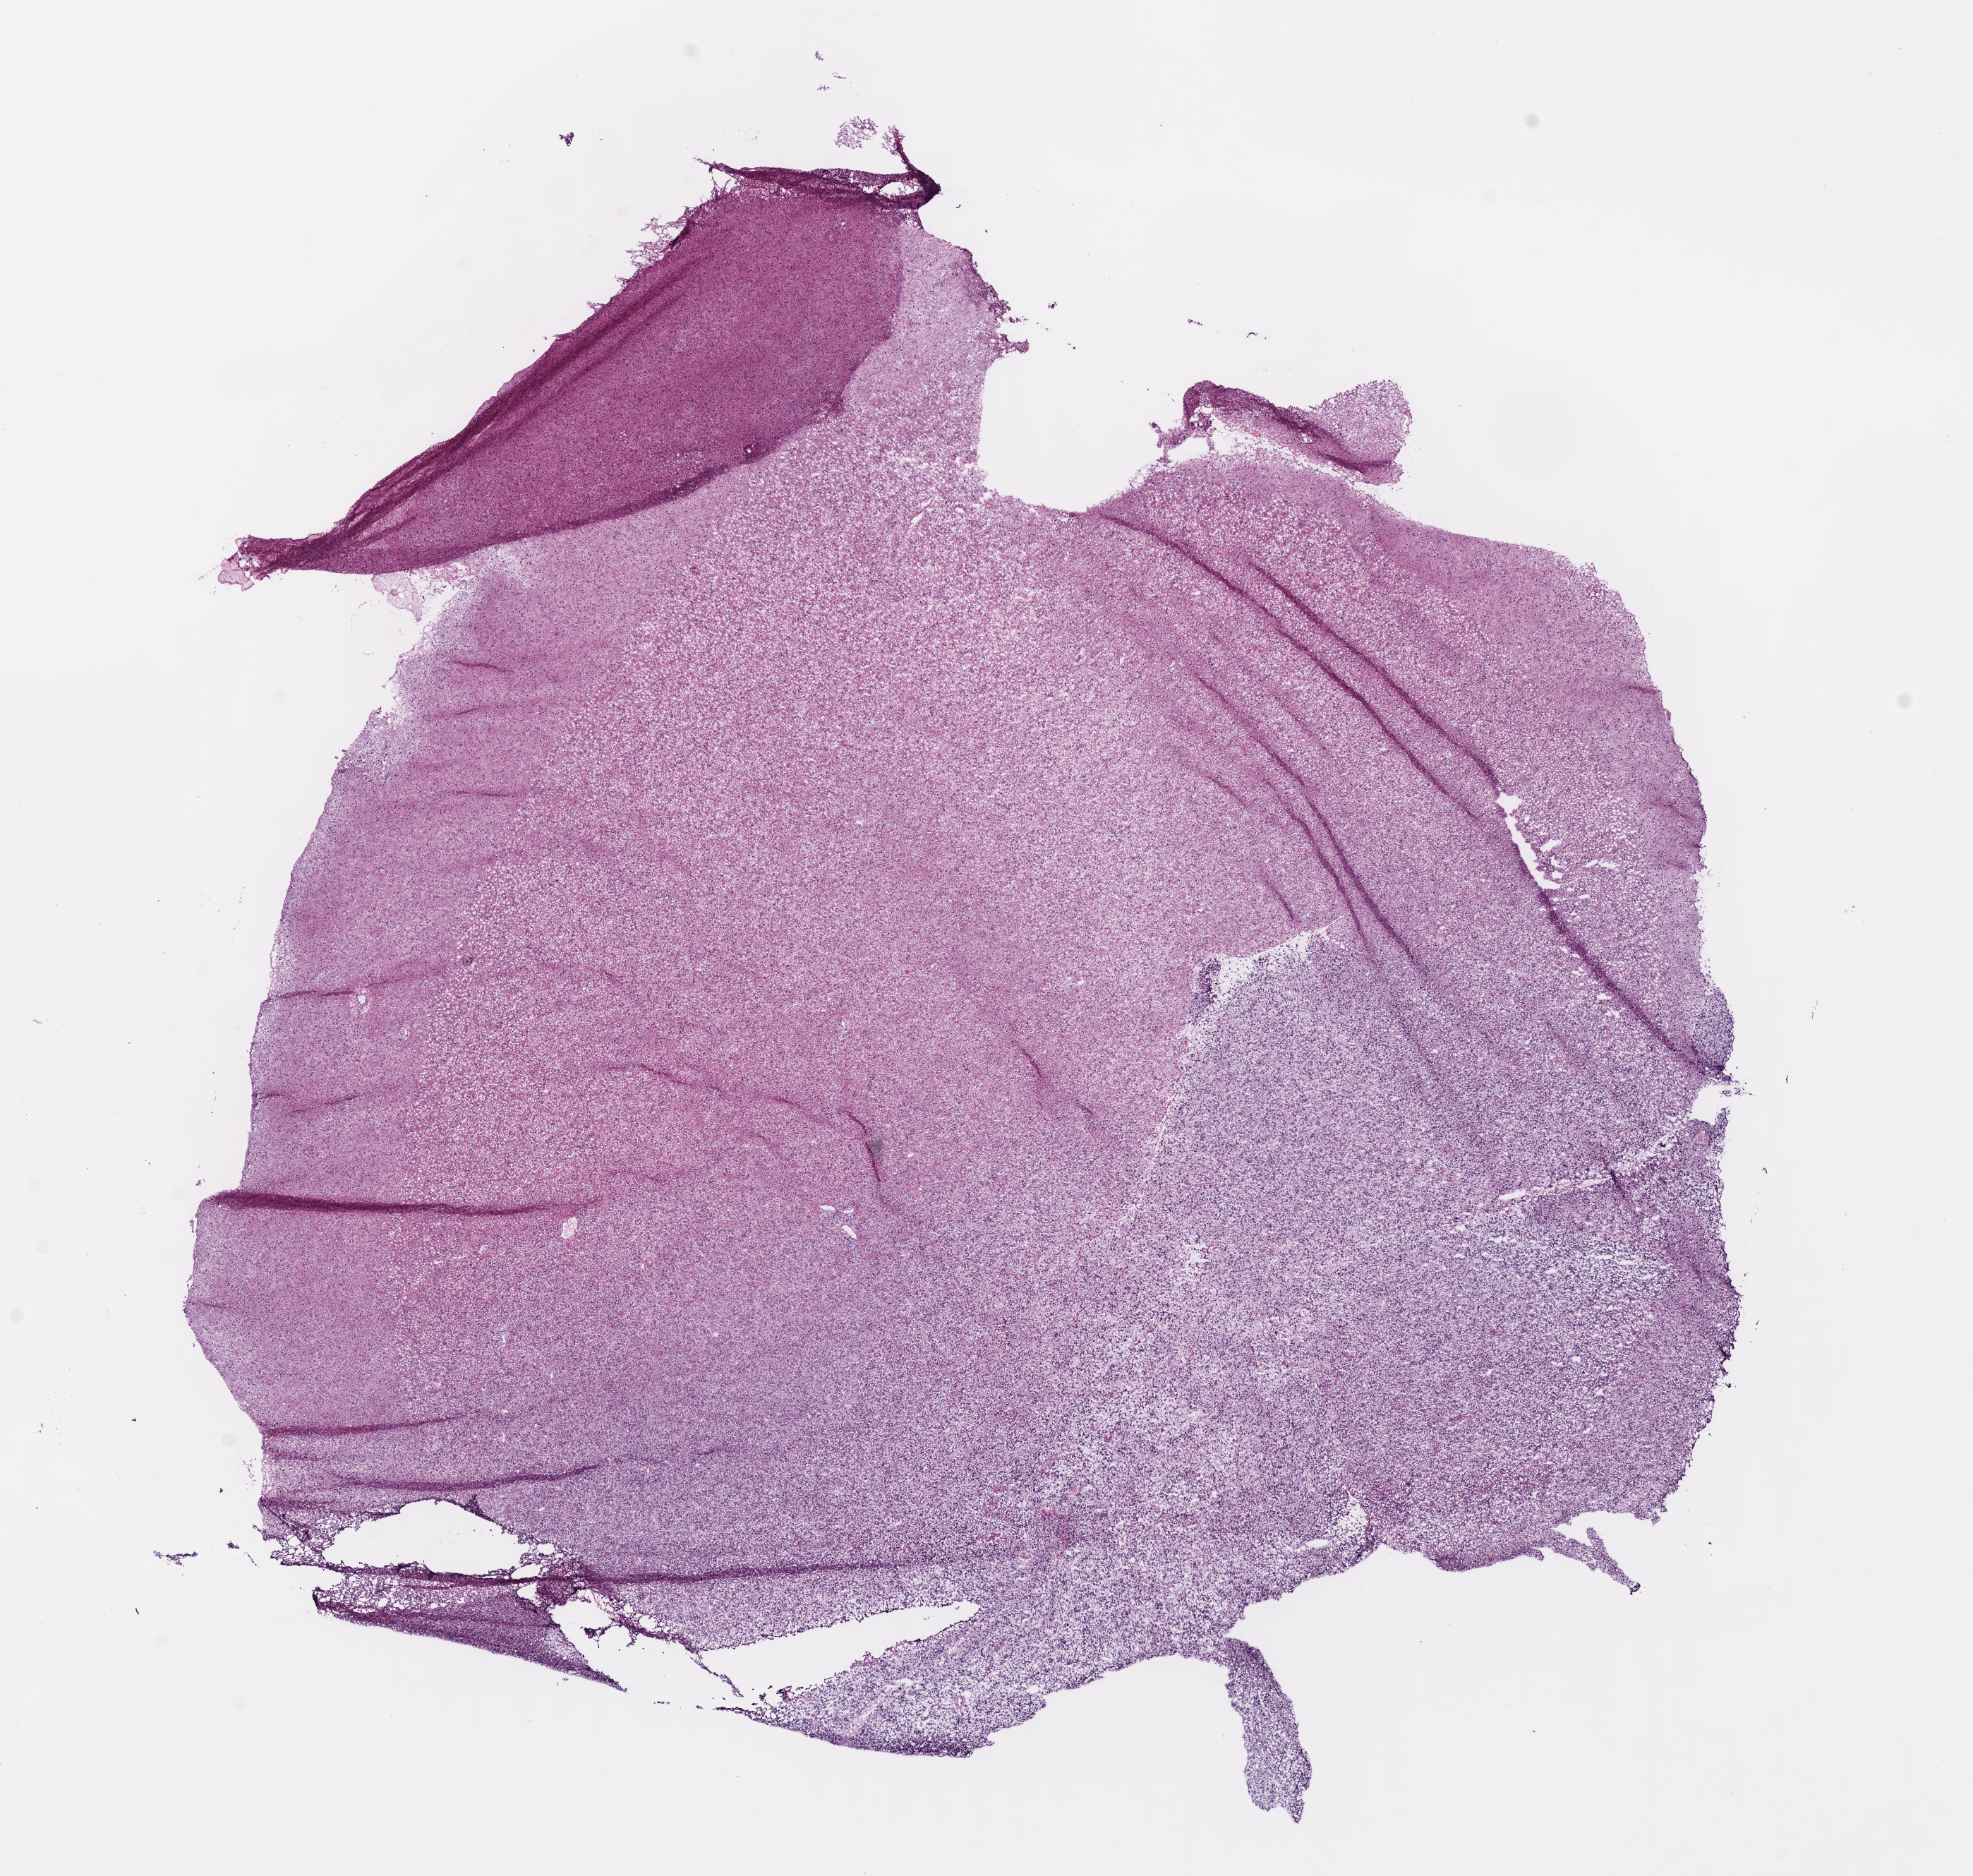
Digitized Hematoxylin and eosin (H&E) stained tissue section (whole slide), shown as a low-resolution overview of the whole scanned area (about 11.0 x 10.5 mm), frozen section from the bottom of the tissue portion, brain, primary tumour sample. Female, age 30 years at initial diagnosis. Histologic grade: G2 (moderately differentiated). Pathologist review of this section (percent, as recorded): tumour cells 100%, tumour nuclei 70%, normal cells 0%, stromal cells 0%, necrosis 0%.
Pathologic diagnosis: Astrocytoma, NOS.